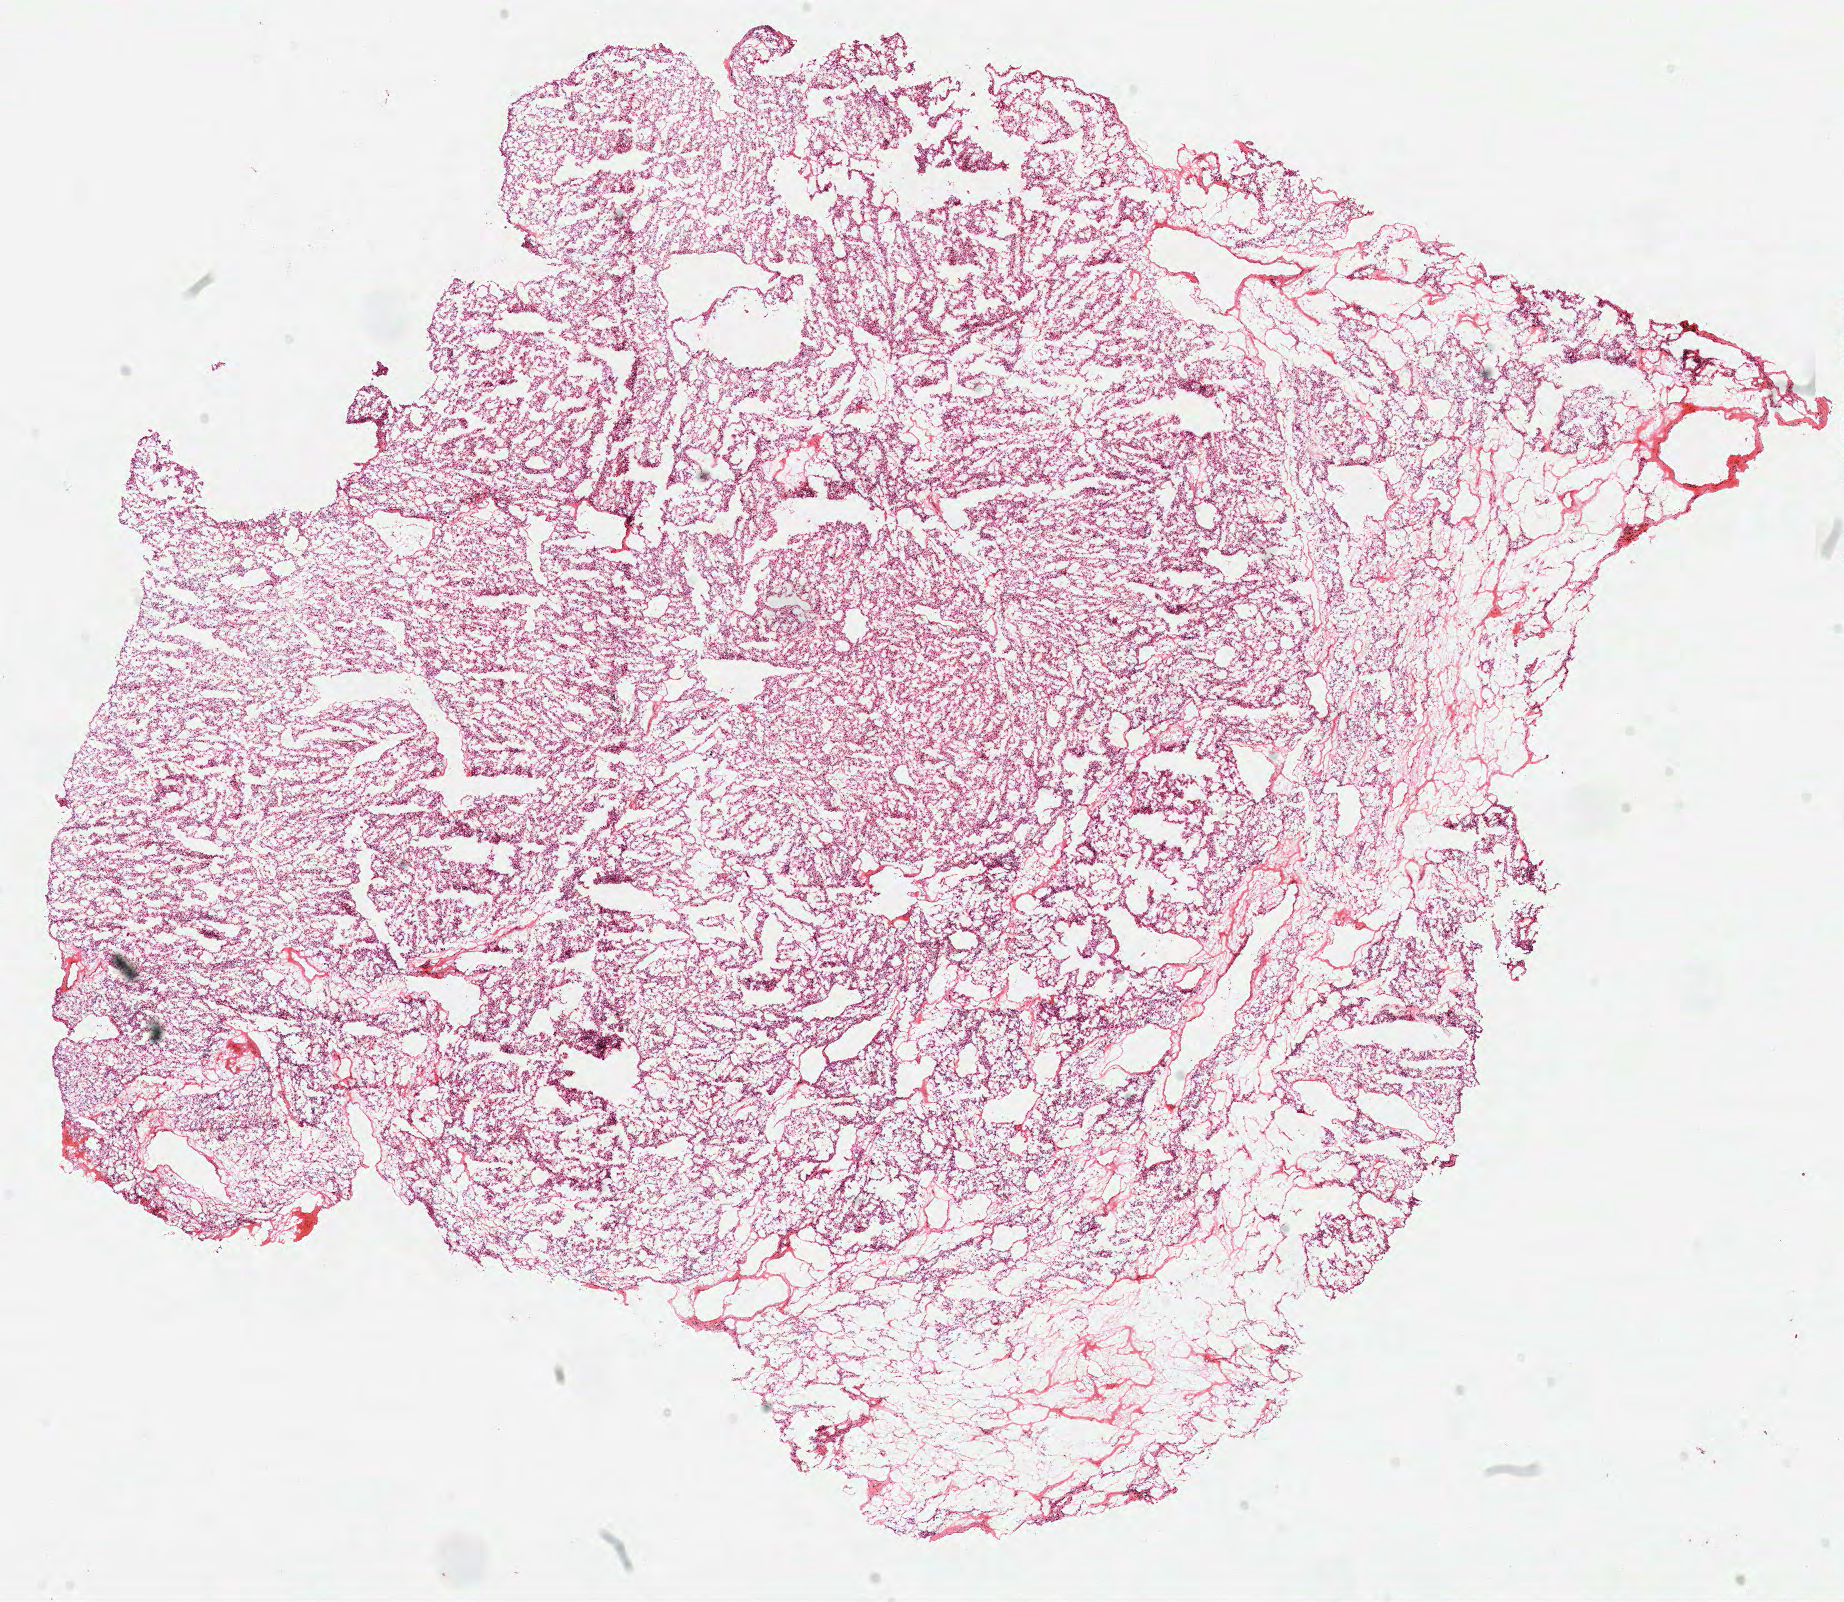
Whole-slide histology image, Hematoxylin and eosin (H&E) stained — a low-resolution overview of the entire scanned area, about 14.5 x 12.6 mm (acquisition: 40x scan); frozen section from the top of the tissue portion; kidney, primary tumour sample. Patient: female, age at initial diagnosis 59 years. Histologic grade: G2 (moderately differentiated). Pathologist review of this section (percent, as recorded): tumour cells 90%, tumour nuclei 85%, normal cells 0%, stromal cells 10%, necrosis 0%.
* pathologic diagnosis: Clear cell adenocarcinoma, NOS
* AJCC pathologic stage: I